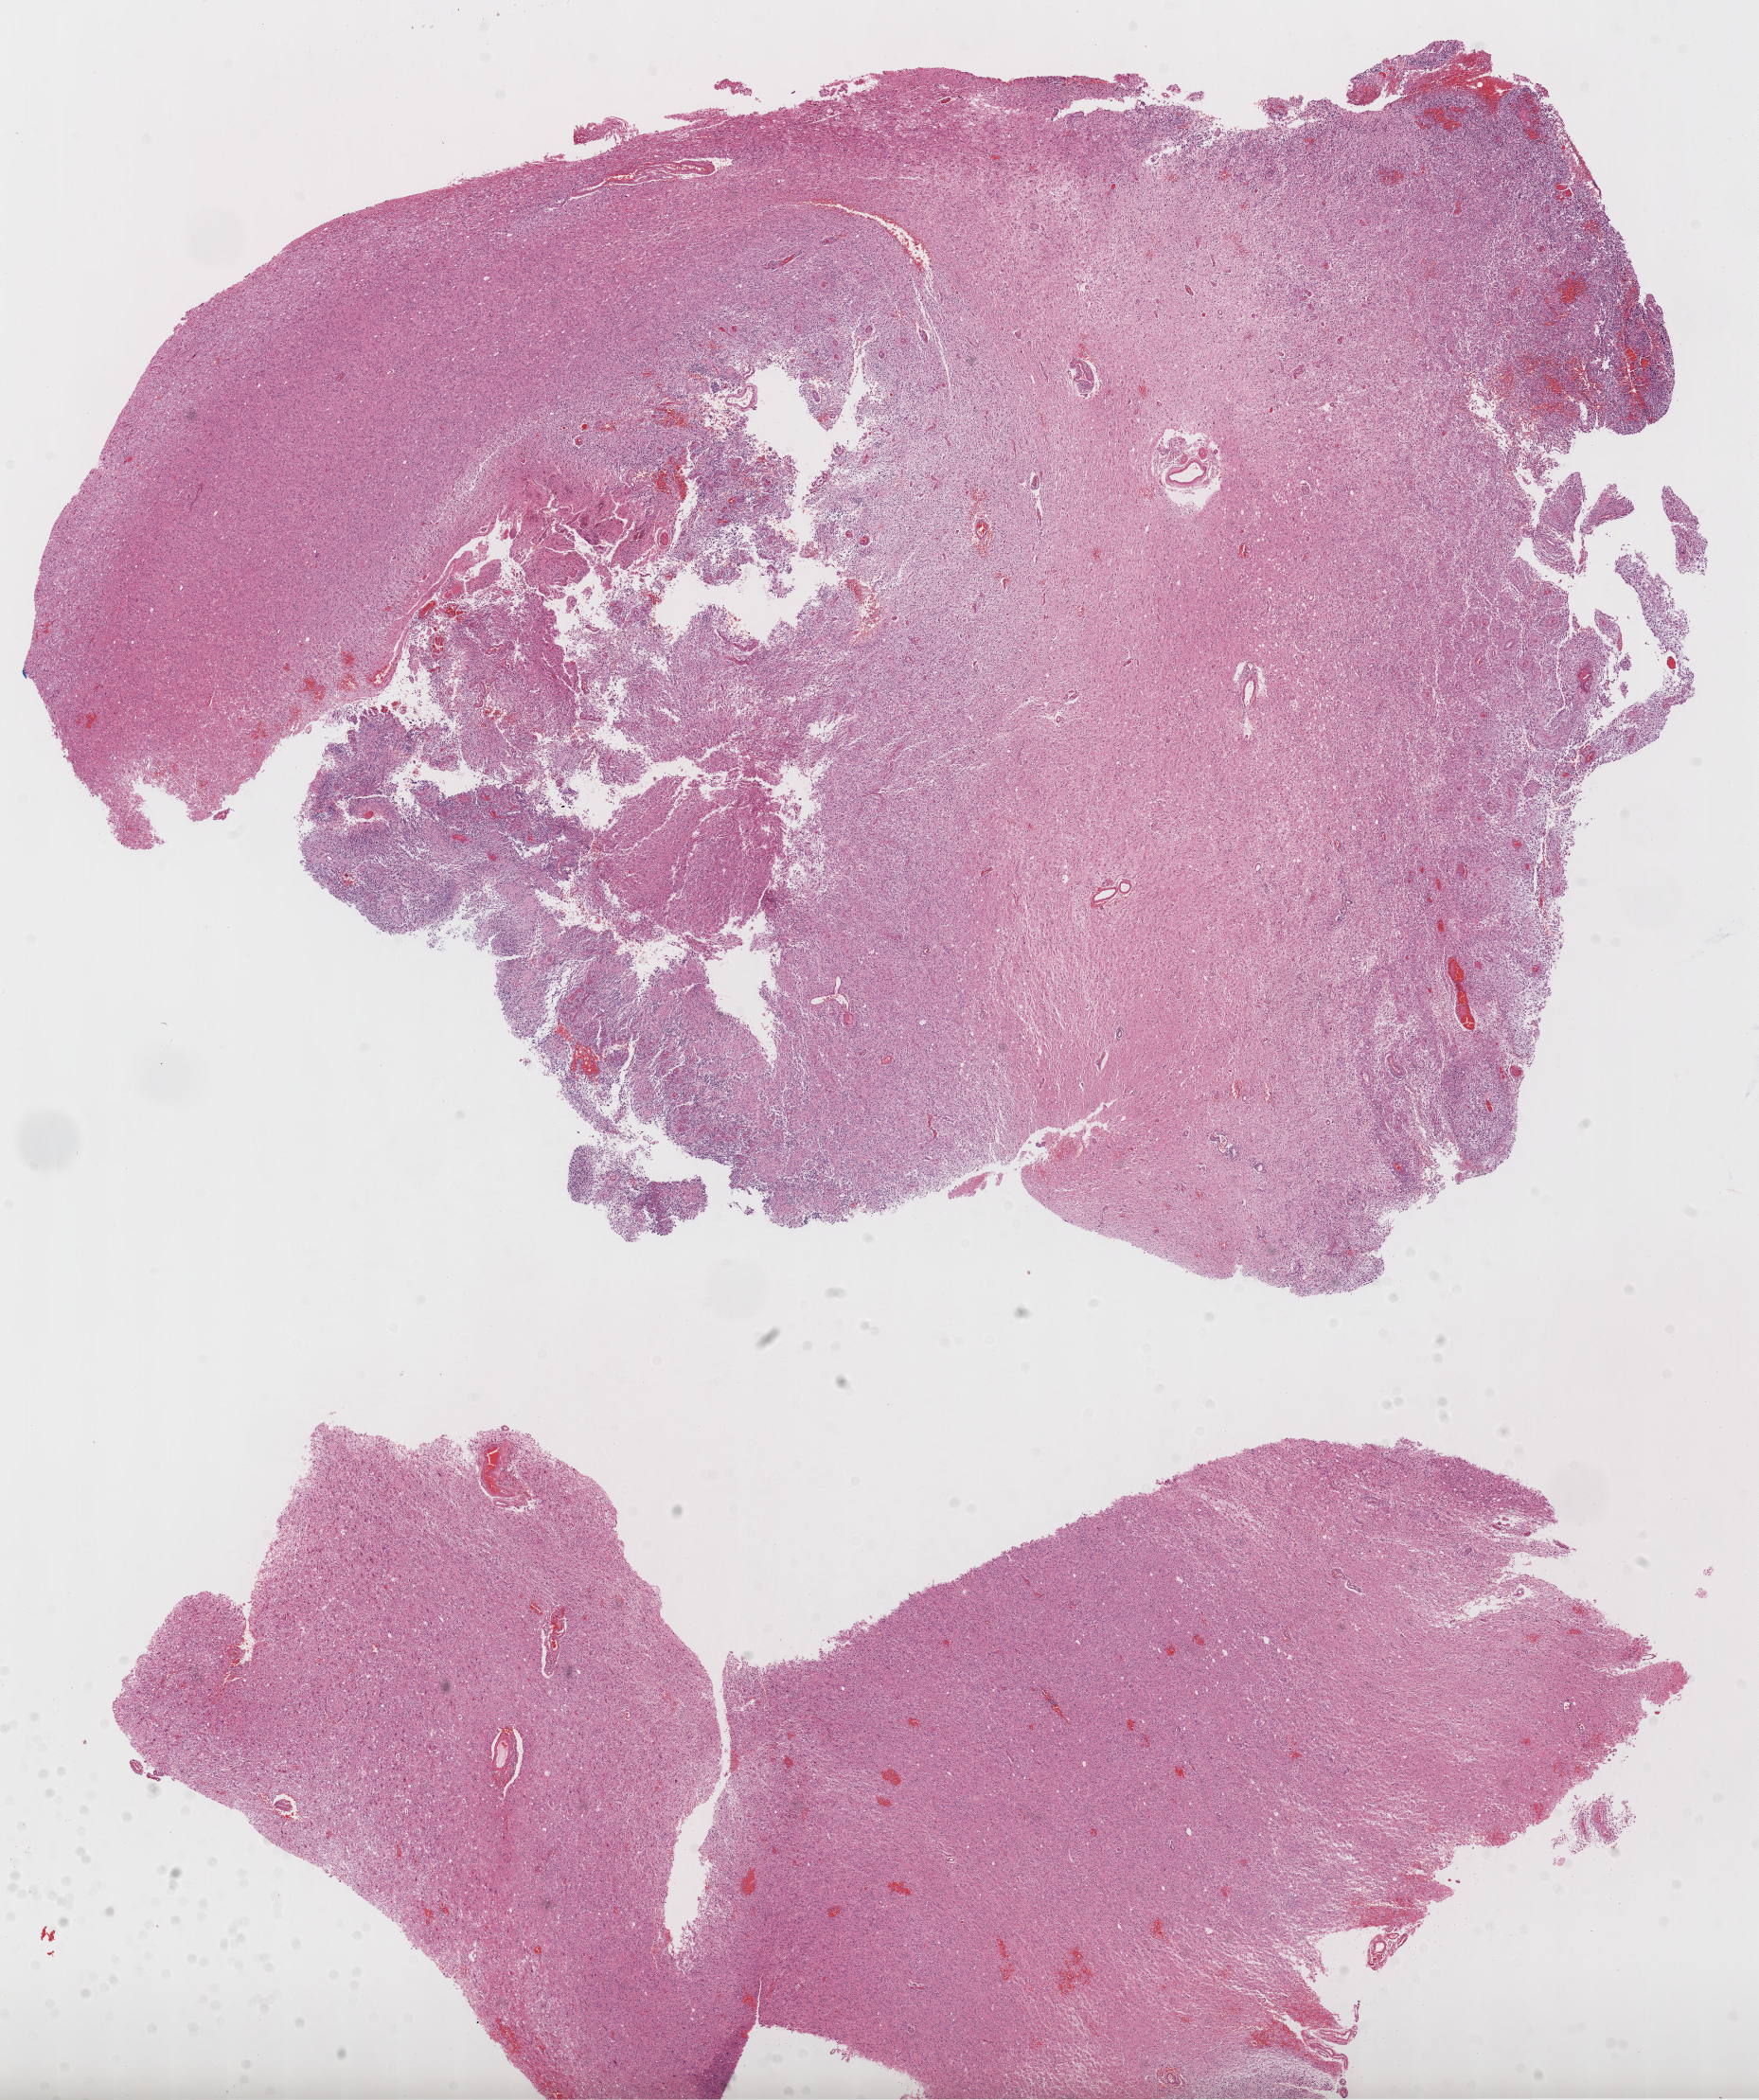
Digitized H&E-stained tissue section (whole slide), whole scanned area (about 15.0 x 17.9 mm, acquisition: 20x scan) shown as a low-resolution overview; formalin-fixed paraffin-embedded (FFPE) diagnostic section; sample: primary tumour, brain. Patient: male, age at initial diagnosis 51 years.
Diagnosis: Glioblastoma.